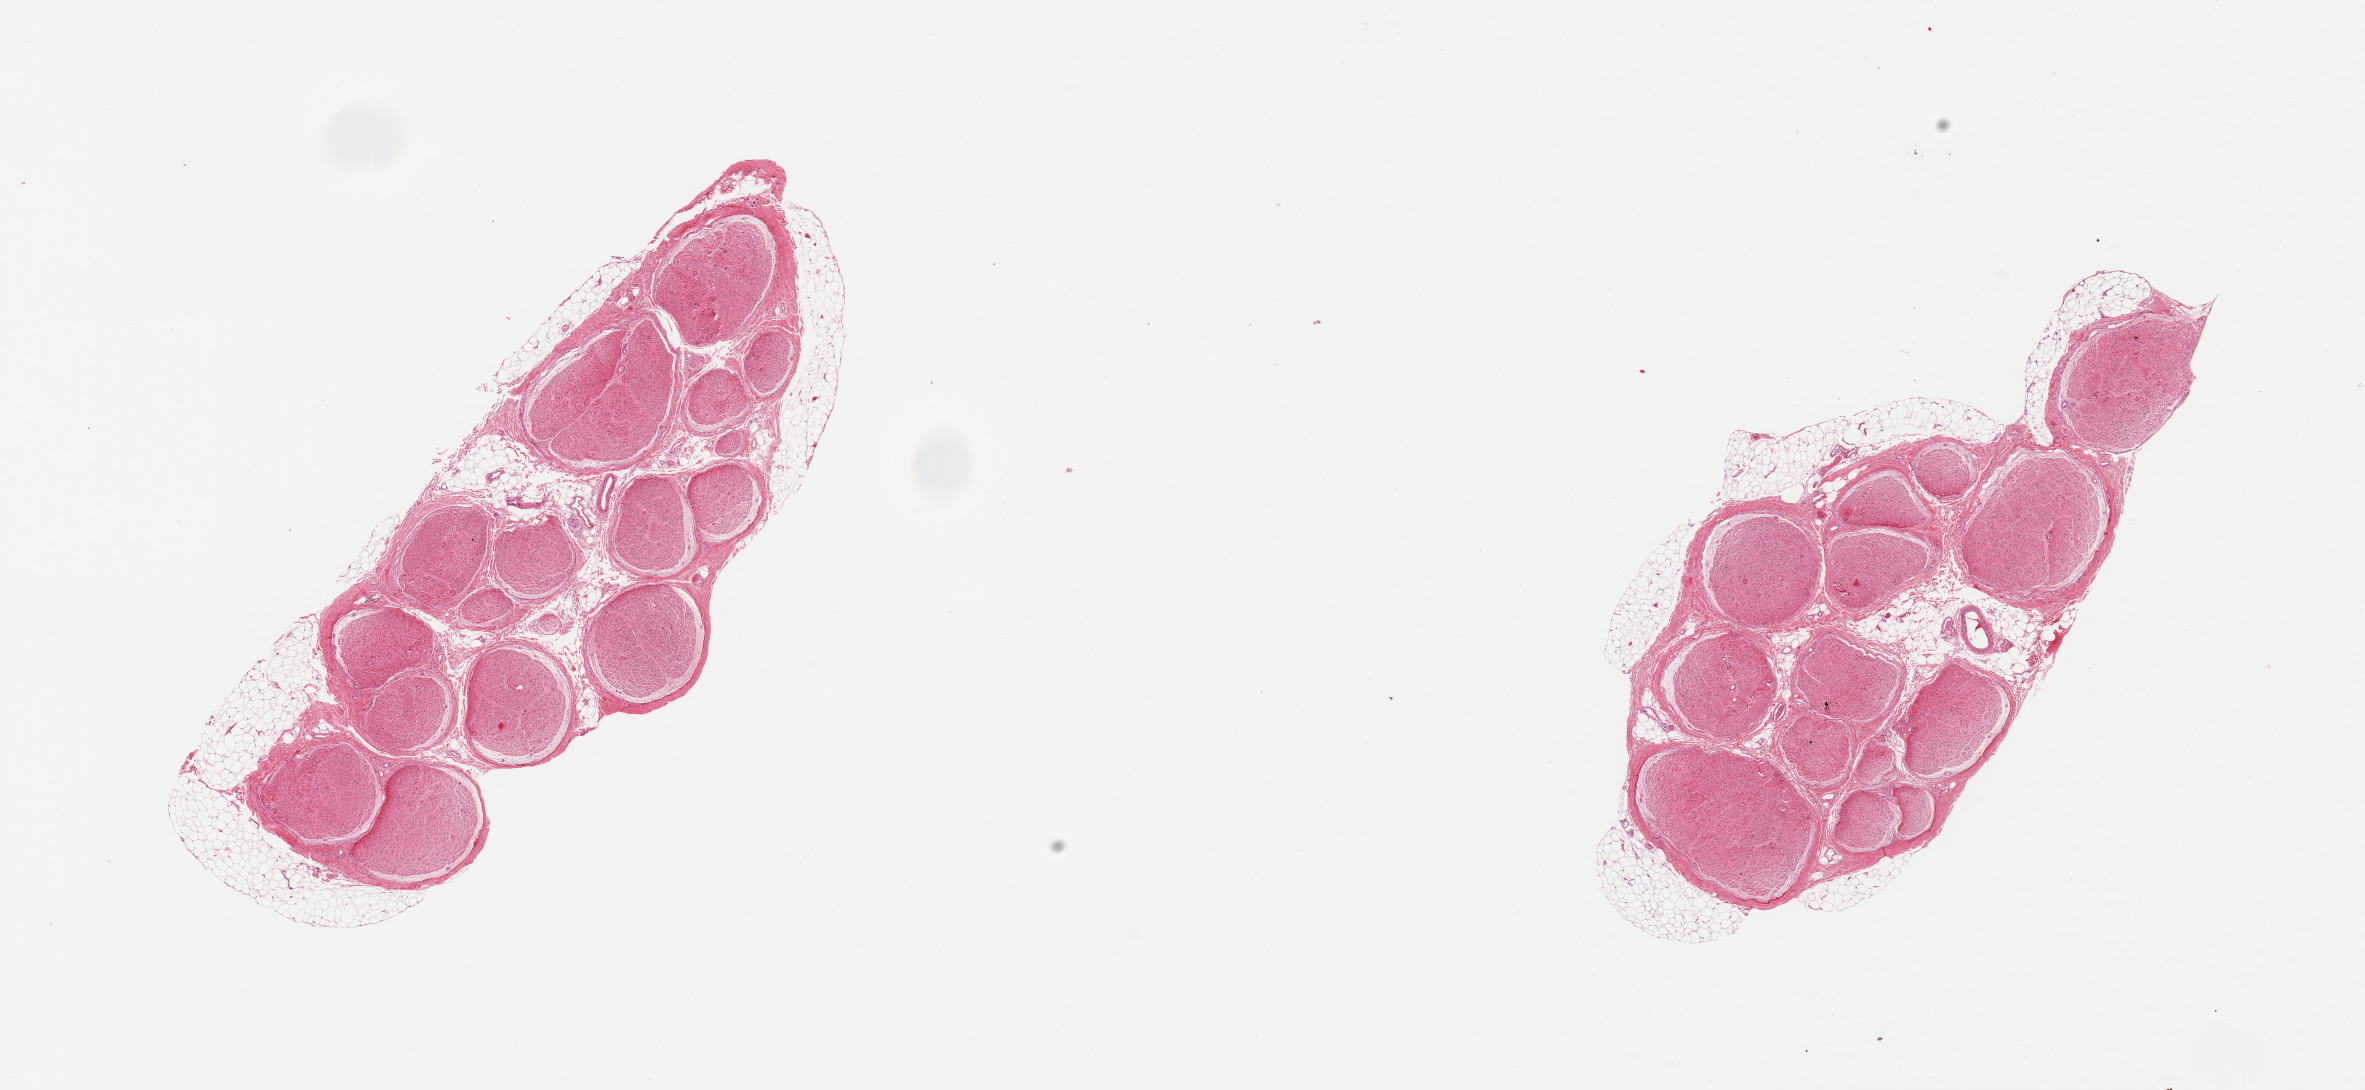
Digitized haematoxylin and eosin-stained section — shown as a low-resolution overview of the whole scanned area (about 18.7 x 8.6 mm, slide scanned at 20x), PAXgene-fixed, paraffin-embedded tissue, target tissue: tibial nerve, tissue donor sample. Donor sex: female.
* pathologist's review note for this sample: 2 pieces; well trimmed; 10% internal and external fat